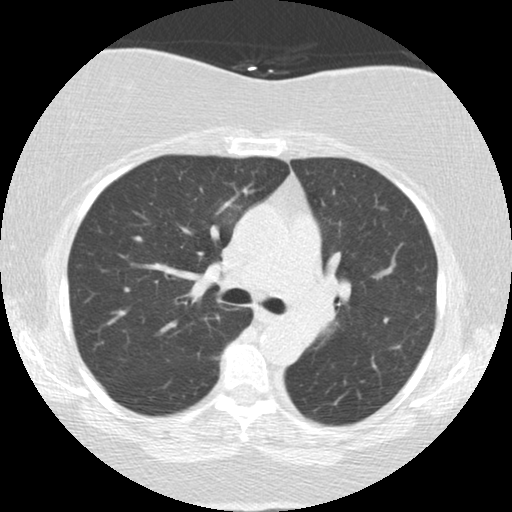
Low-dose screening chest CT, one axial slice; position 85 of 136 along the scan axis; lung window (W 1500 / L -600 HU); 2.5 mm slice thickness; 512 × 512 image matrix, field of view 309 × 309 mm.
Annotated regions visible in this slice (manually delineated by an expert):
- lesion 2 (tumor, mediastinum): bounding box (x1, y1, x2, y2) in pixels: (296, 276, 338, 338)